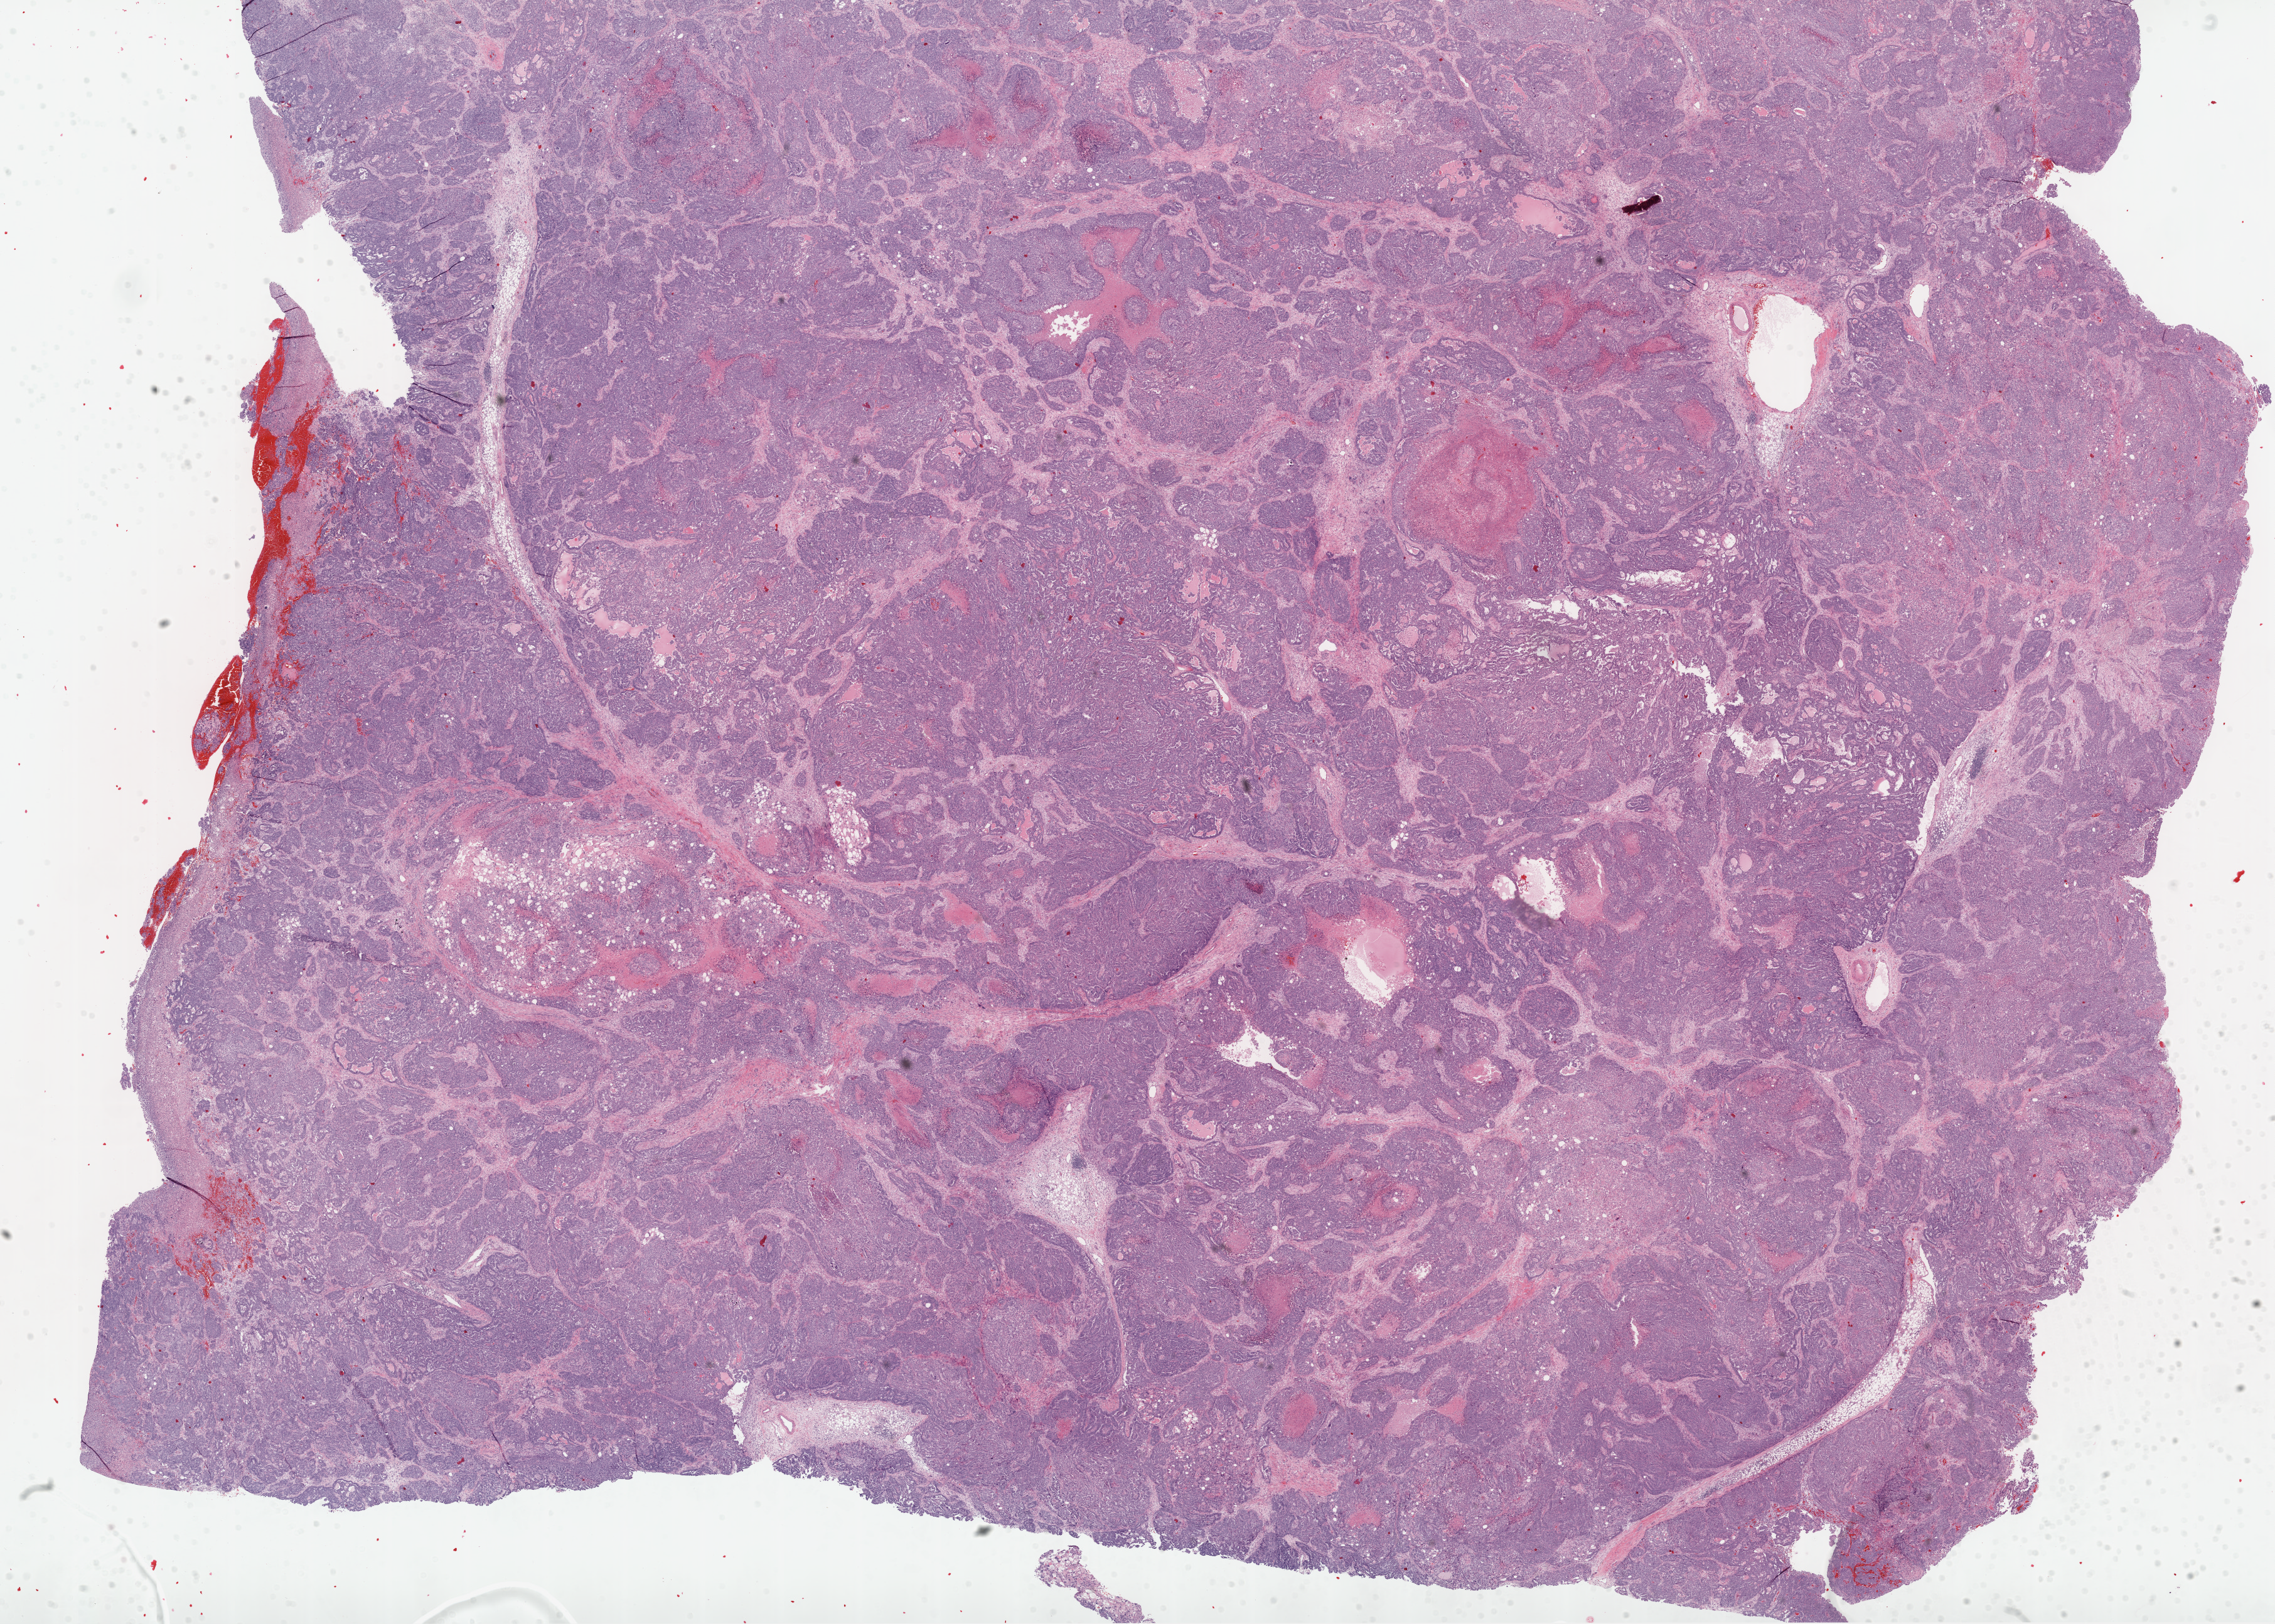
Digitized Hematoxylin and eosin (H&E) stained tissue section (whole slide) — shown as a low-resolution overview of the whole scanned area (about 29.1 x 20.8 mm, slide scanned at 20x); frozen section; ovary, primary tumour sample. Patient: female, age at initial diagnosis 58 years. Histologic grade: G3 (poorly differentiated). Pathologist review of this section (percent, as recorded): tumour cells 80%, tumour nuclei 90%, normal cells 0%, stromal cells 12%, necrosis 8%.
FIGO stage: IIIC. Diagnosis: Serous cystadenocarcinoma, NOS.